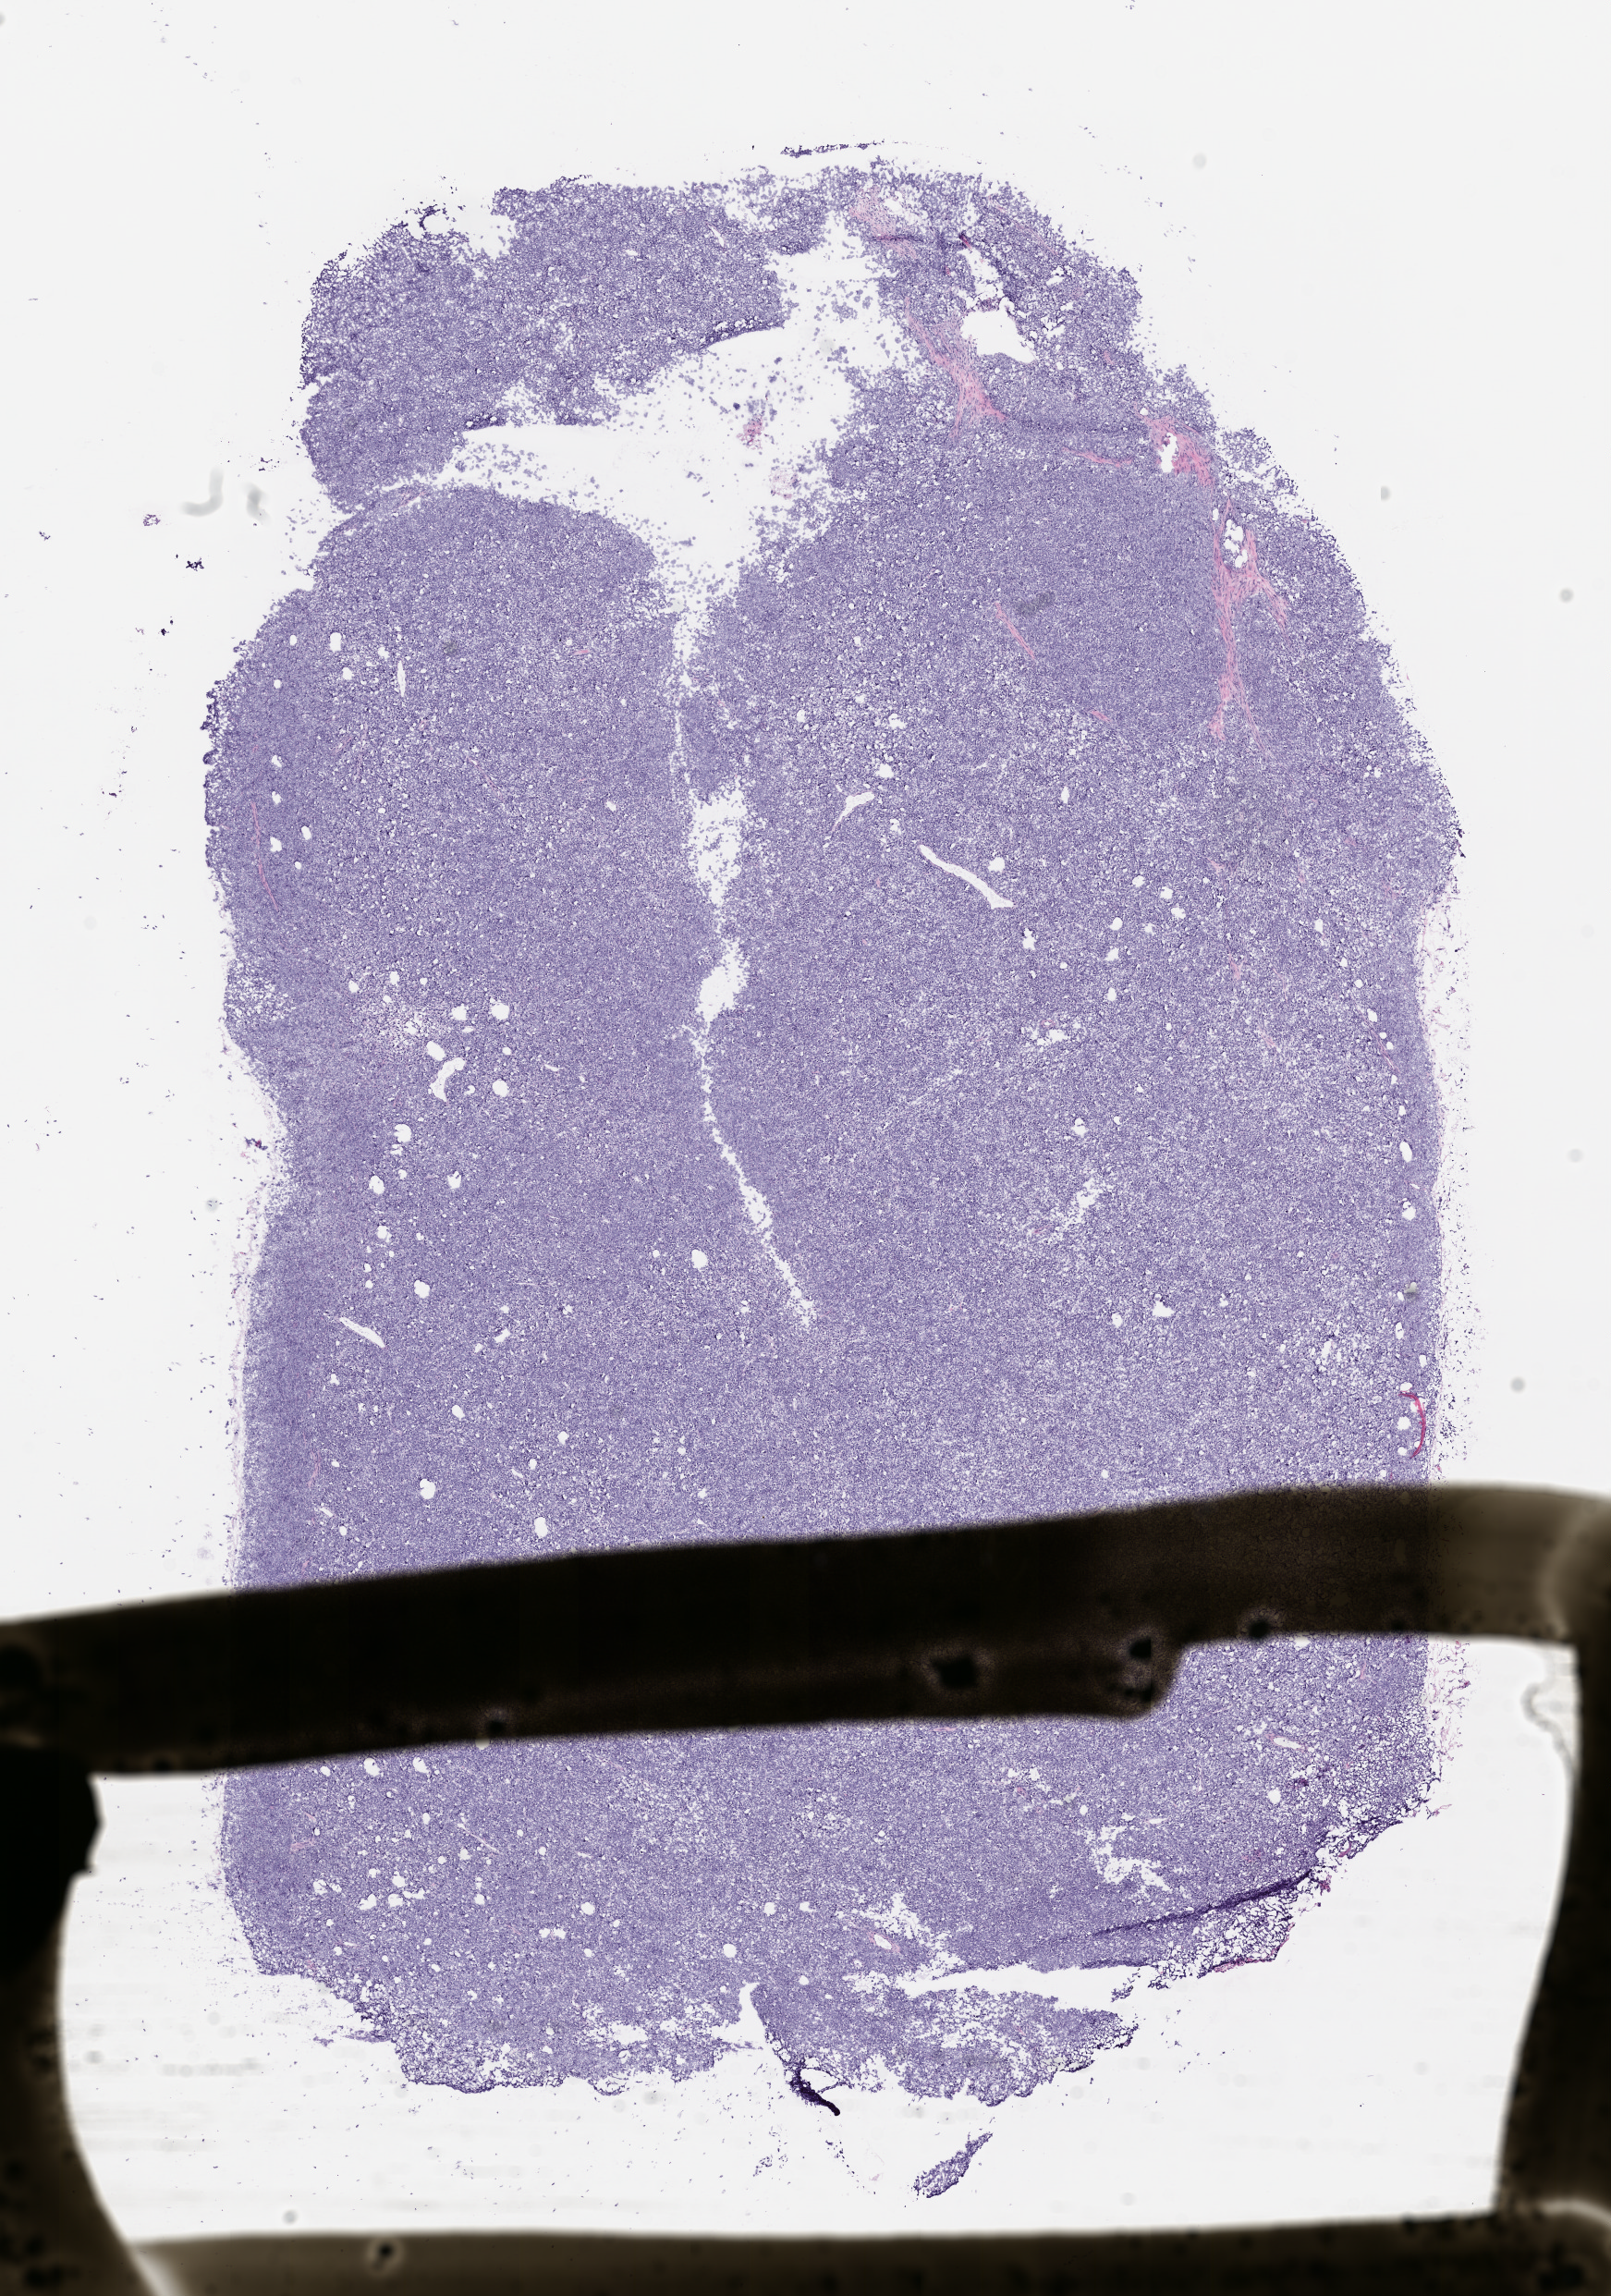
Whole-slide image, haematoxylin and eosin: patient-derived xenograft (human tumor grown in a mouse), passage 1, a low-resolution overview of the entire scanned area, about 7.0 x 10.0 mm. Formalin-fixed, paraffin-embedded (FFPE) tissue. Tumor site category: musculoskeletal.
Originating patient diagnosis: Synovial Sarcoma.